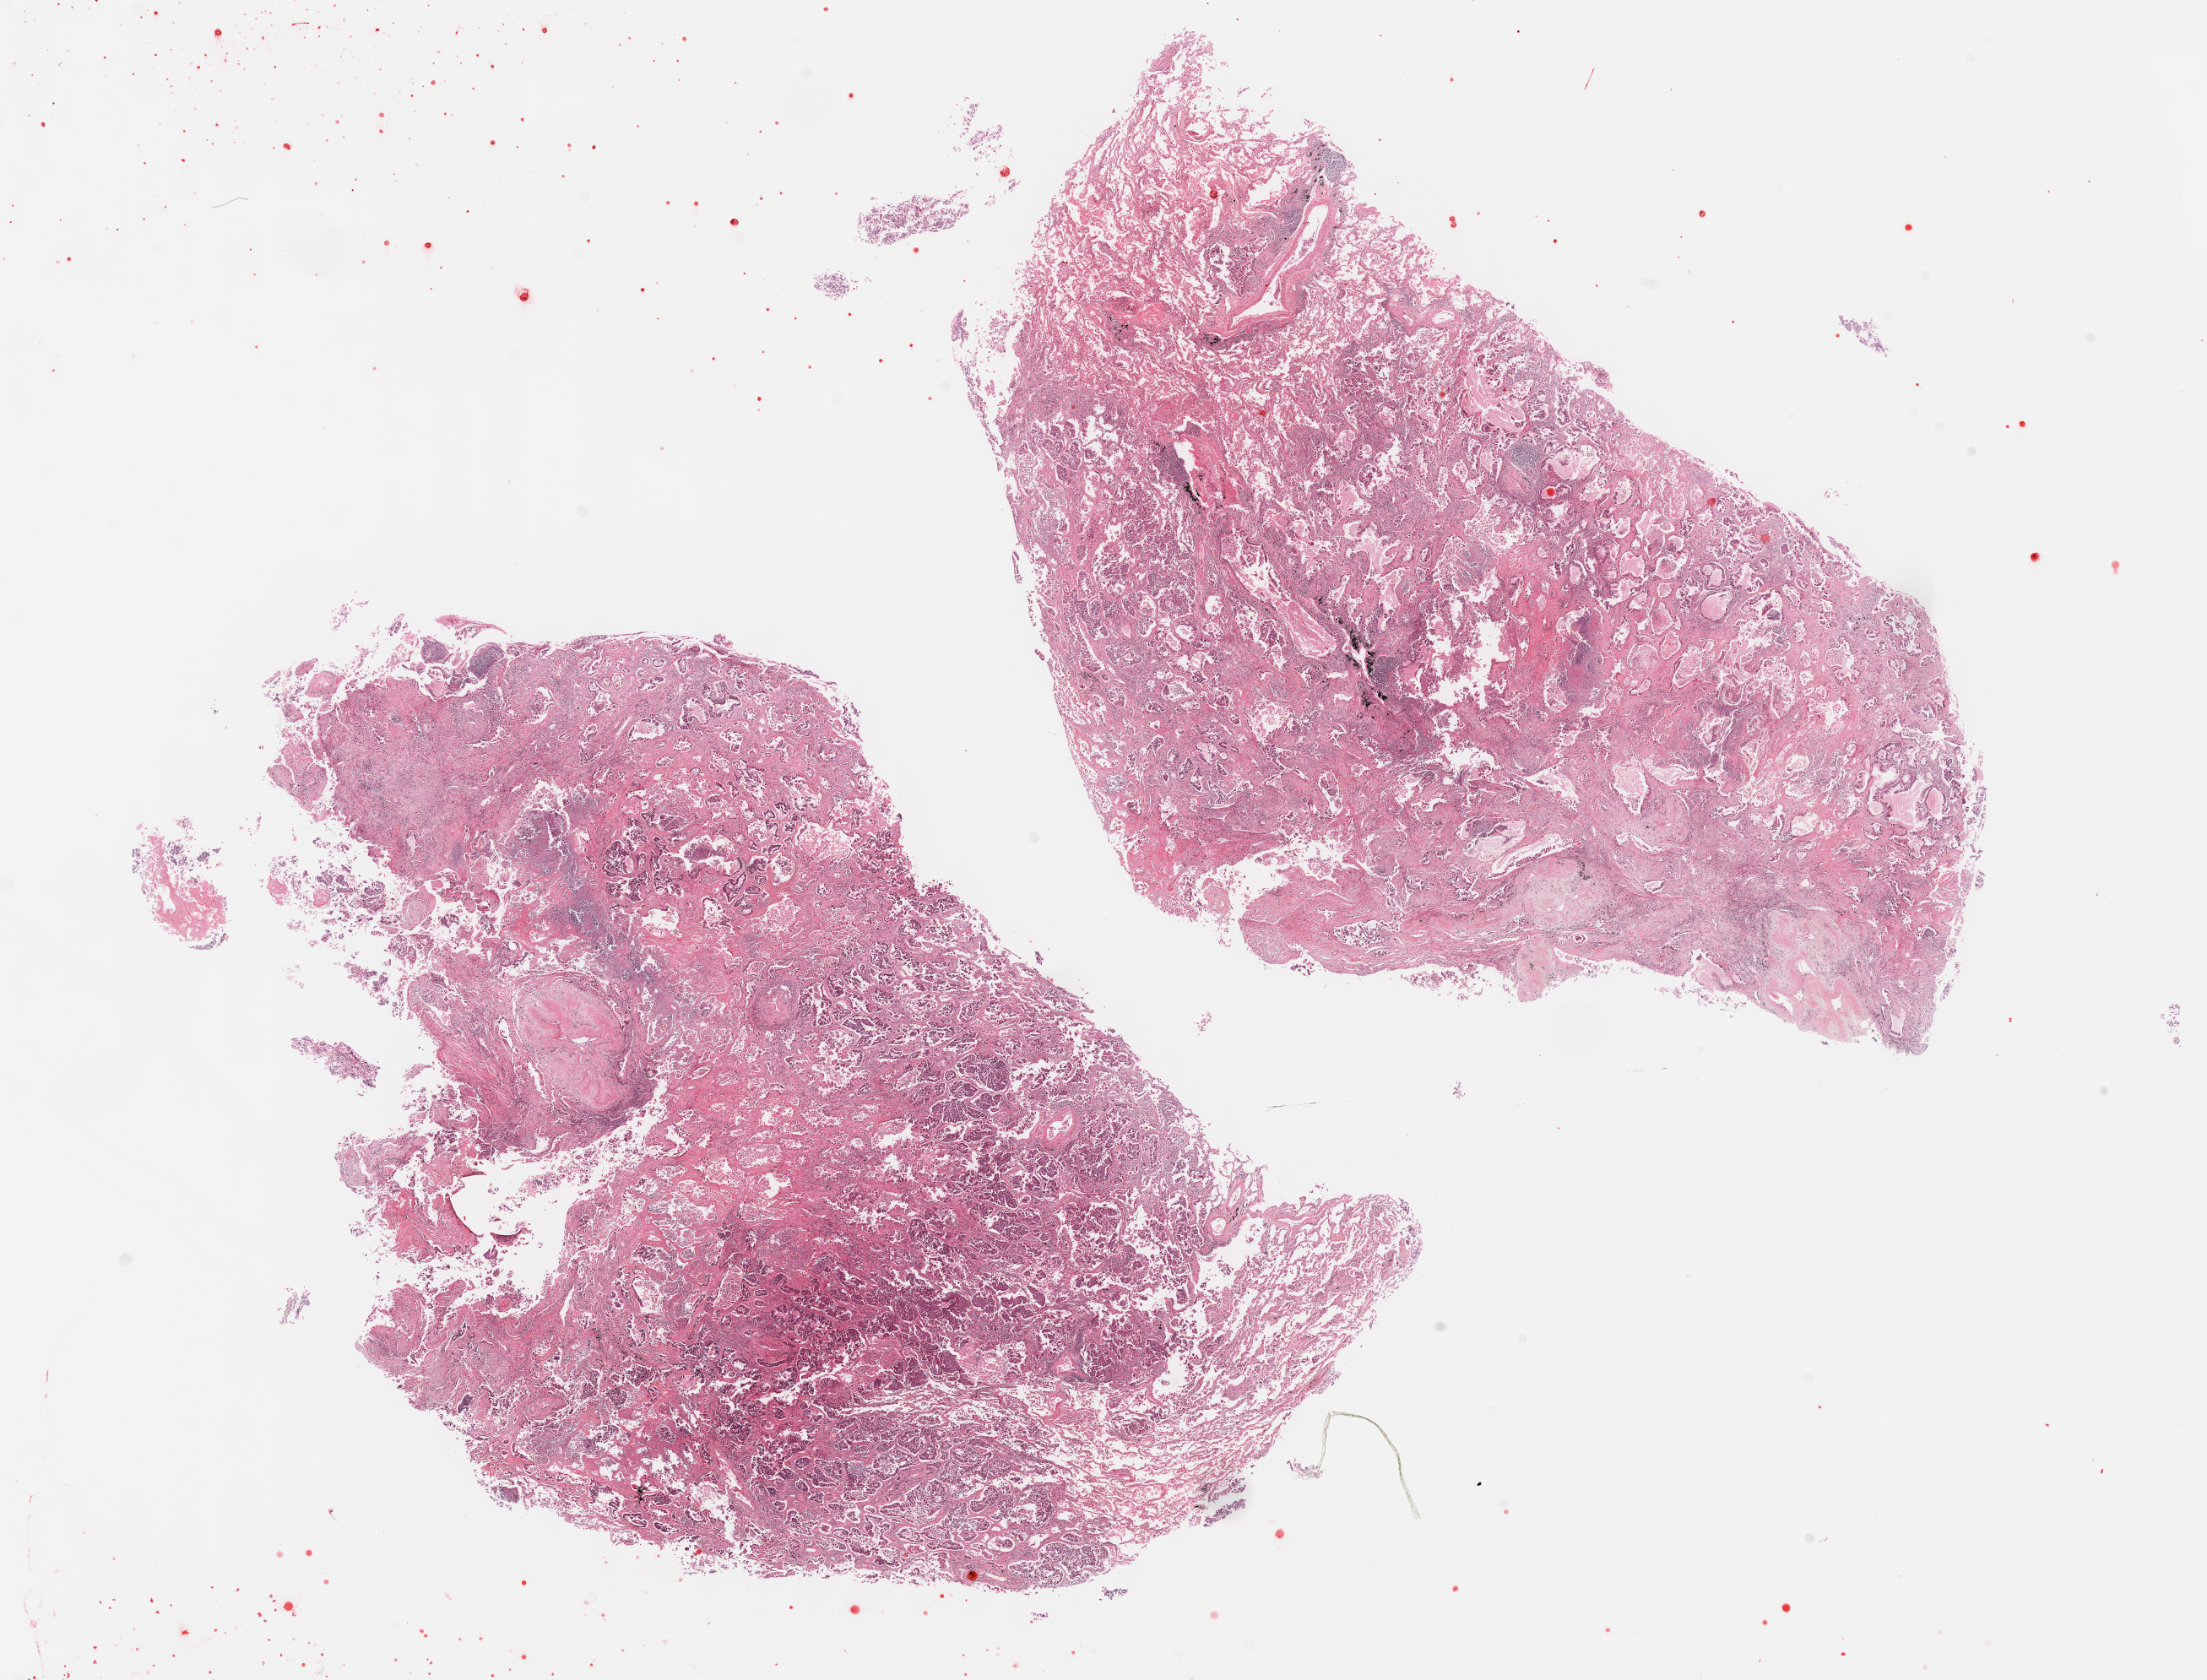
H&E whole-slide image — whole scanned area (about 21.1 x 16.1 mm) shown as a low-resolution overview. FFPE section. Lung, primary tumour sample. Patient: female, age at initial diagnosis 77 years.
- diagnosis: Adenocarcinoma, NOS (upper lobe, lung)
- laterality: right
- AJCC pathologic stage: IIIA
- TNM: T2 N2 M0